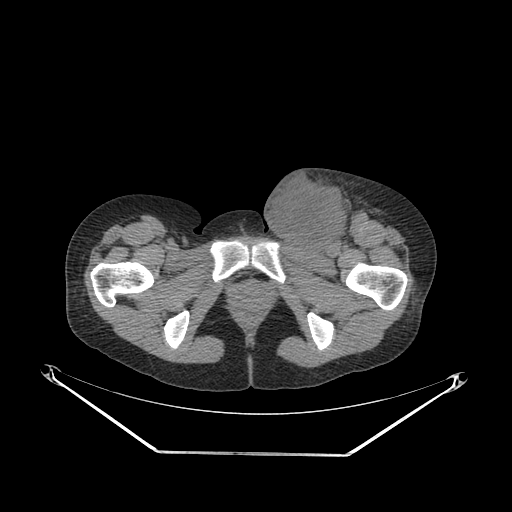
CT of an extremity soft-tissue mass (from a PET/CT study), one axial slice. Position 61 of 267 along the scan axis. 140 kVp. Soft-tissue window (W 400 / L 40 HU). 3.75 mm slice thickness. 512 × 512 image matrix. Female patient. From the clinical record (not read from this slice): histological type: leiomyosarcoma; grade: high; site of the primary tumour: groin.
Outlined on this slice (expert contour drawn on MRI and transferred to this co-registered scan by the dataset authors):
- gross tumour volume including surrounding oedema: bounding box [x1, y1, x2, y2] px = [260, 171, 375, 252]
- gross tumour volume (mass): [260, 176, 348, 250]